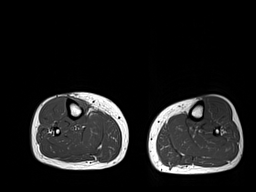
MRI of an extremity soft-tissue mass, one axial slice; position 11 of 32 along the scan axis; 6 mm slice thickness; 256 × 192 image matrix. Female patient. Case-level facts recorded for this patient, not image findings: histological type: undifferentiated – high grade; grade: high; site of the primary tumour: right thigh.
Outlined on this slice (manually delineated by an expert):
- gross tumour volume (mass): bounding box (x1, y1, x2, y2) in pixels: (74, 98, 90, 112)